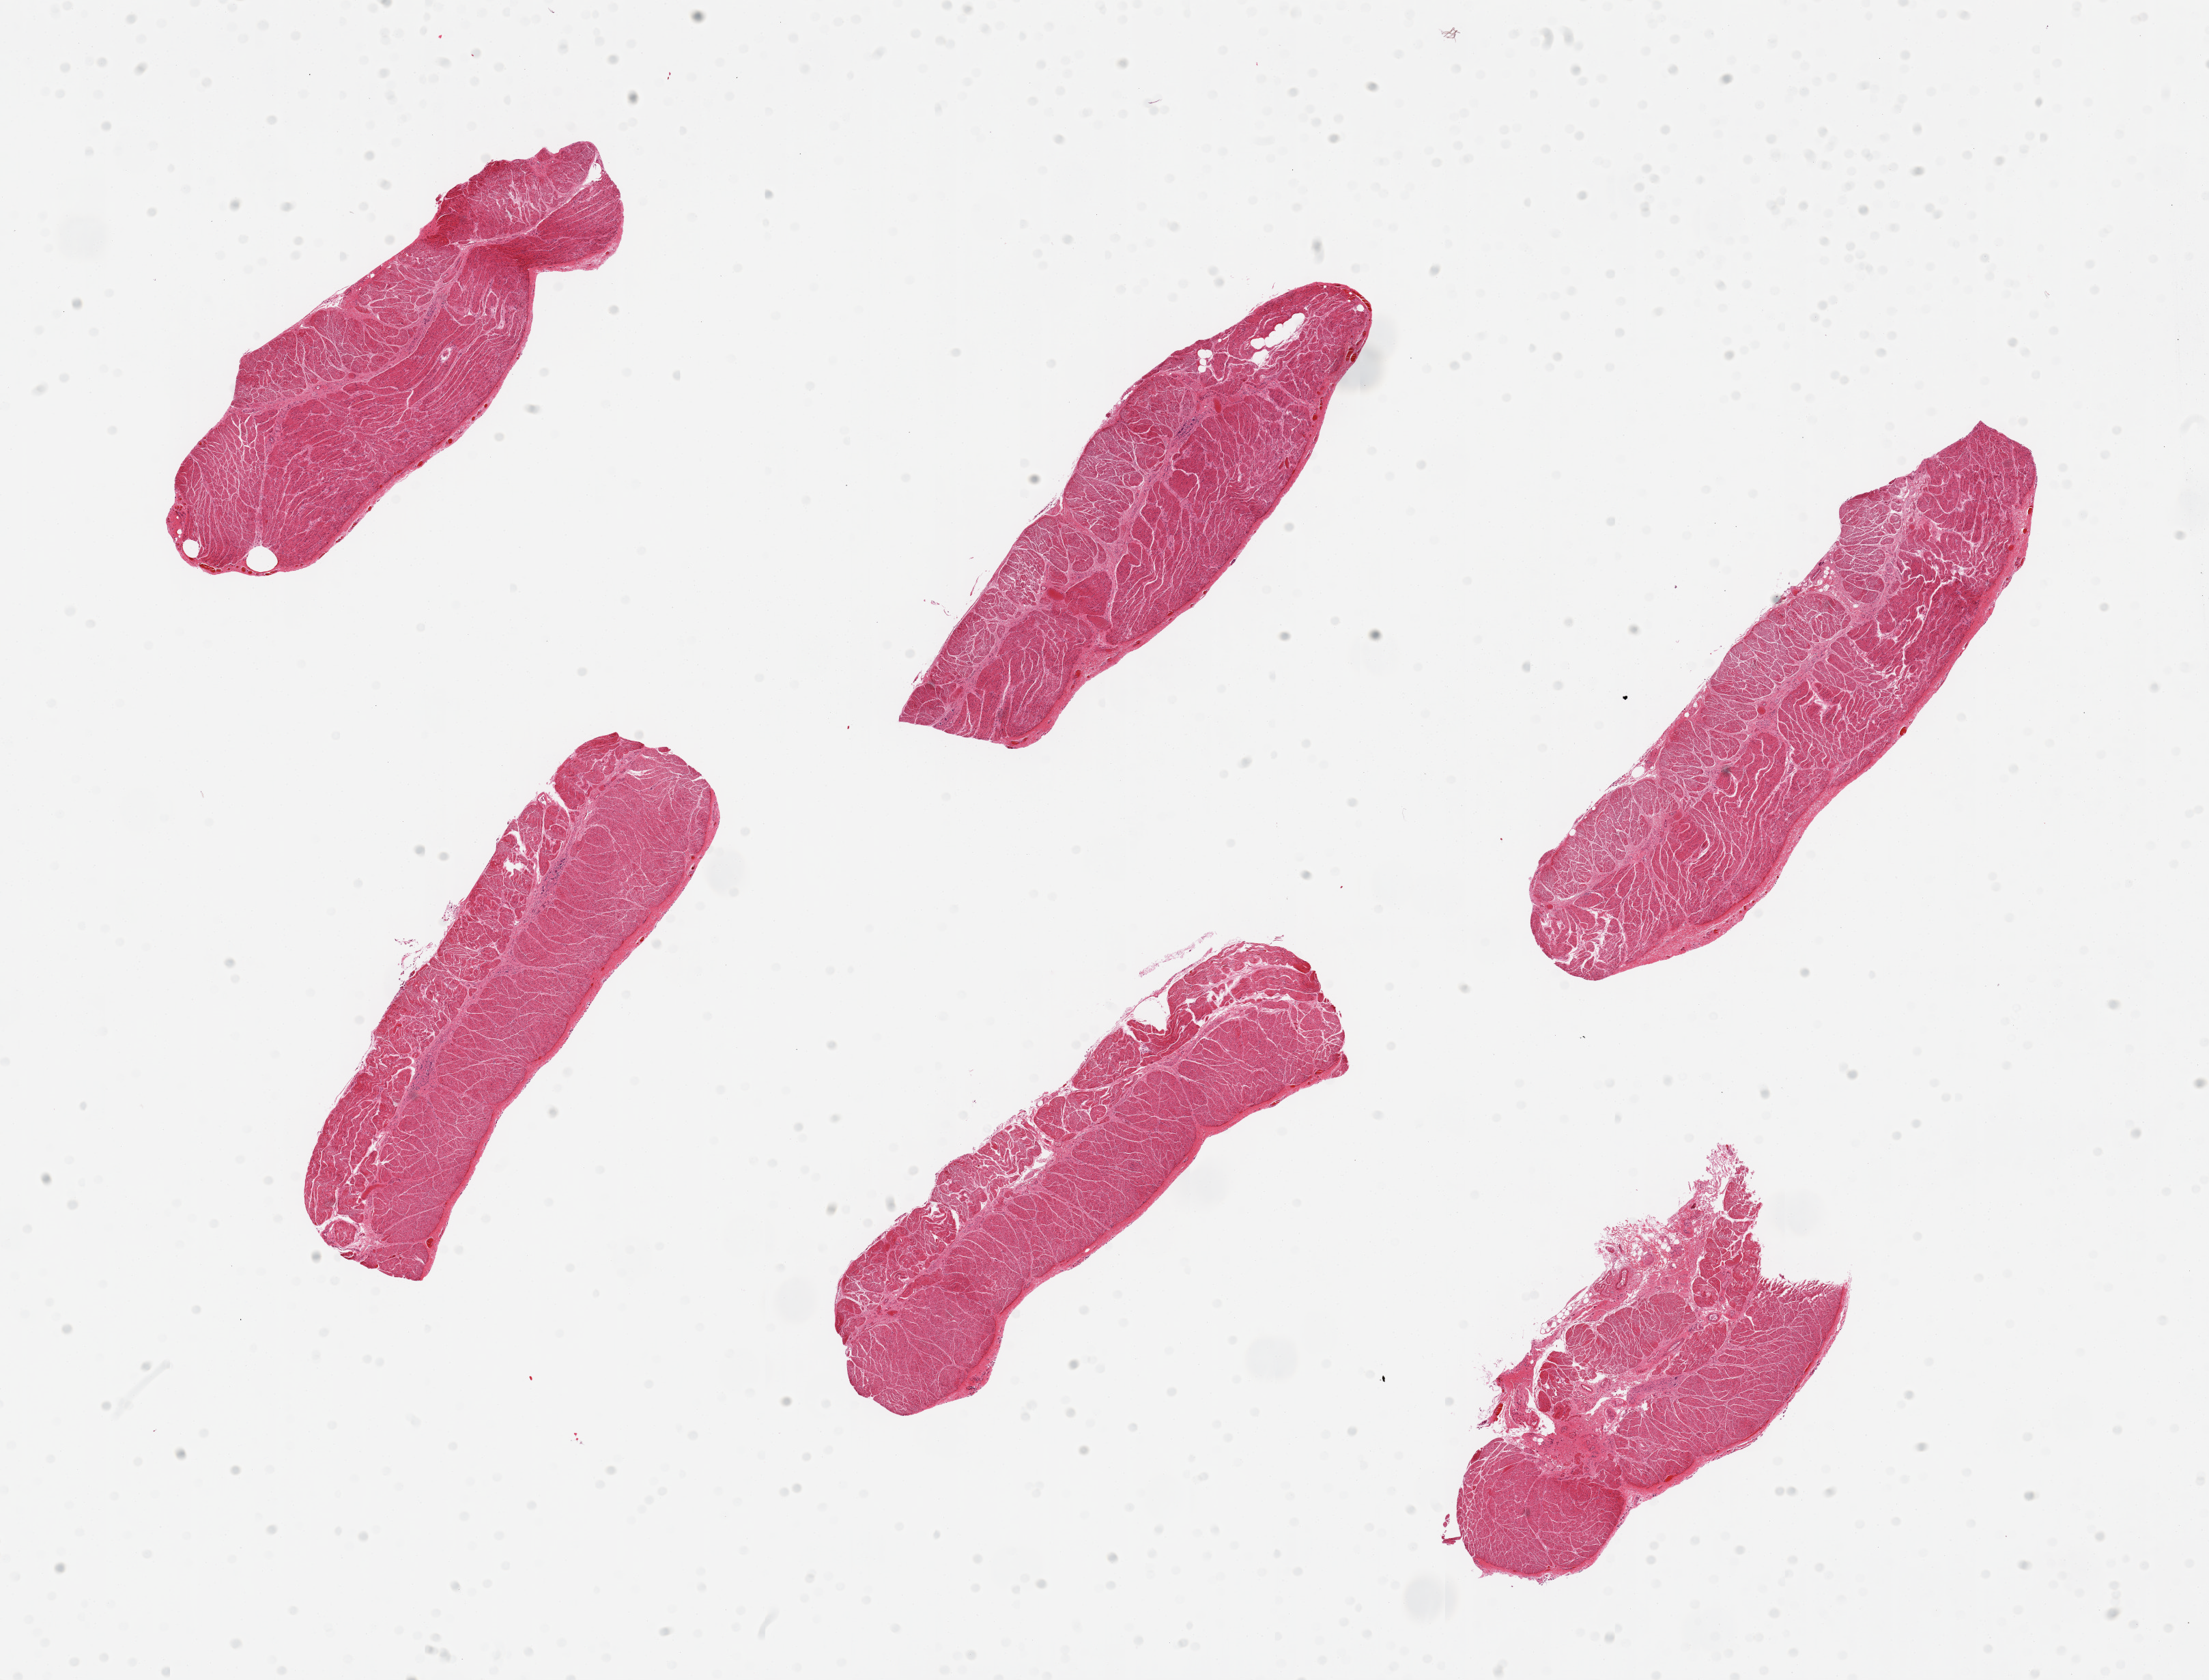
Hematoxylin and eosin (H&E) whole-slide image, brightfield, a low-resolution overview of the entire scanned area, about 25.6 x 19.5 mm (acquisition: 20x scan). PAXgene-fixed paraffin-embedded (PFPE) section. Target tissue: gastroesophageal junction. Tissue donor sample. Donor sex: male.
- reviewer comment on this tissue sample: 6 pieces, well trimmed